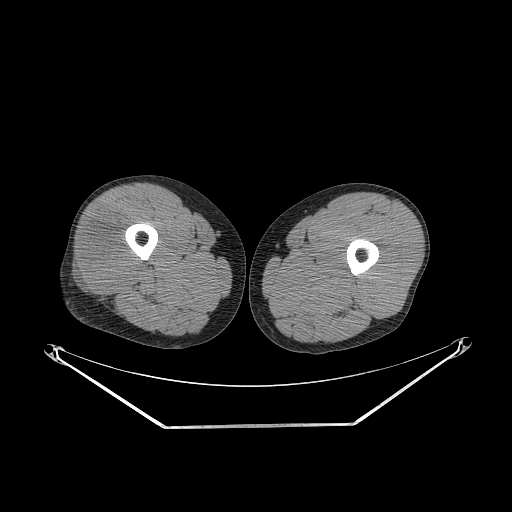
CT of an extremity soft-tissue mass (from a PET/CT study), one axial slice. Slice 238 of 267 in the series (ordered by position). 140 kVp. Soft-tissue window (W 400 / L 40 HU). 3.75 mm slice thickness. 512 × 512 image matrix, field of view 500 × 500 mm. Male patient. From the clinical record (not read from this slice): histological type: poorly differentiated synovial sarcoma; grade: high; site of the primary tumour: right buttock.
Outlined on this slice (expert contour drawn on MRI and transferred to this co-registered scan by the dataset authors):
- gross tumour volume including surrounding oedema: bounding box <75,221,134,291> (left, top, right, bottom; pixels)
- gross tumour volume (mass): <82,226,134,291>